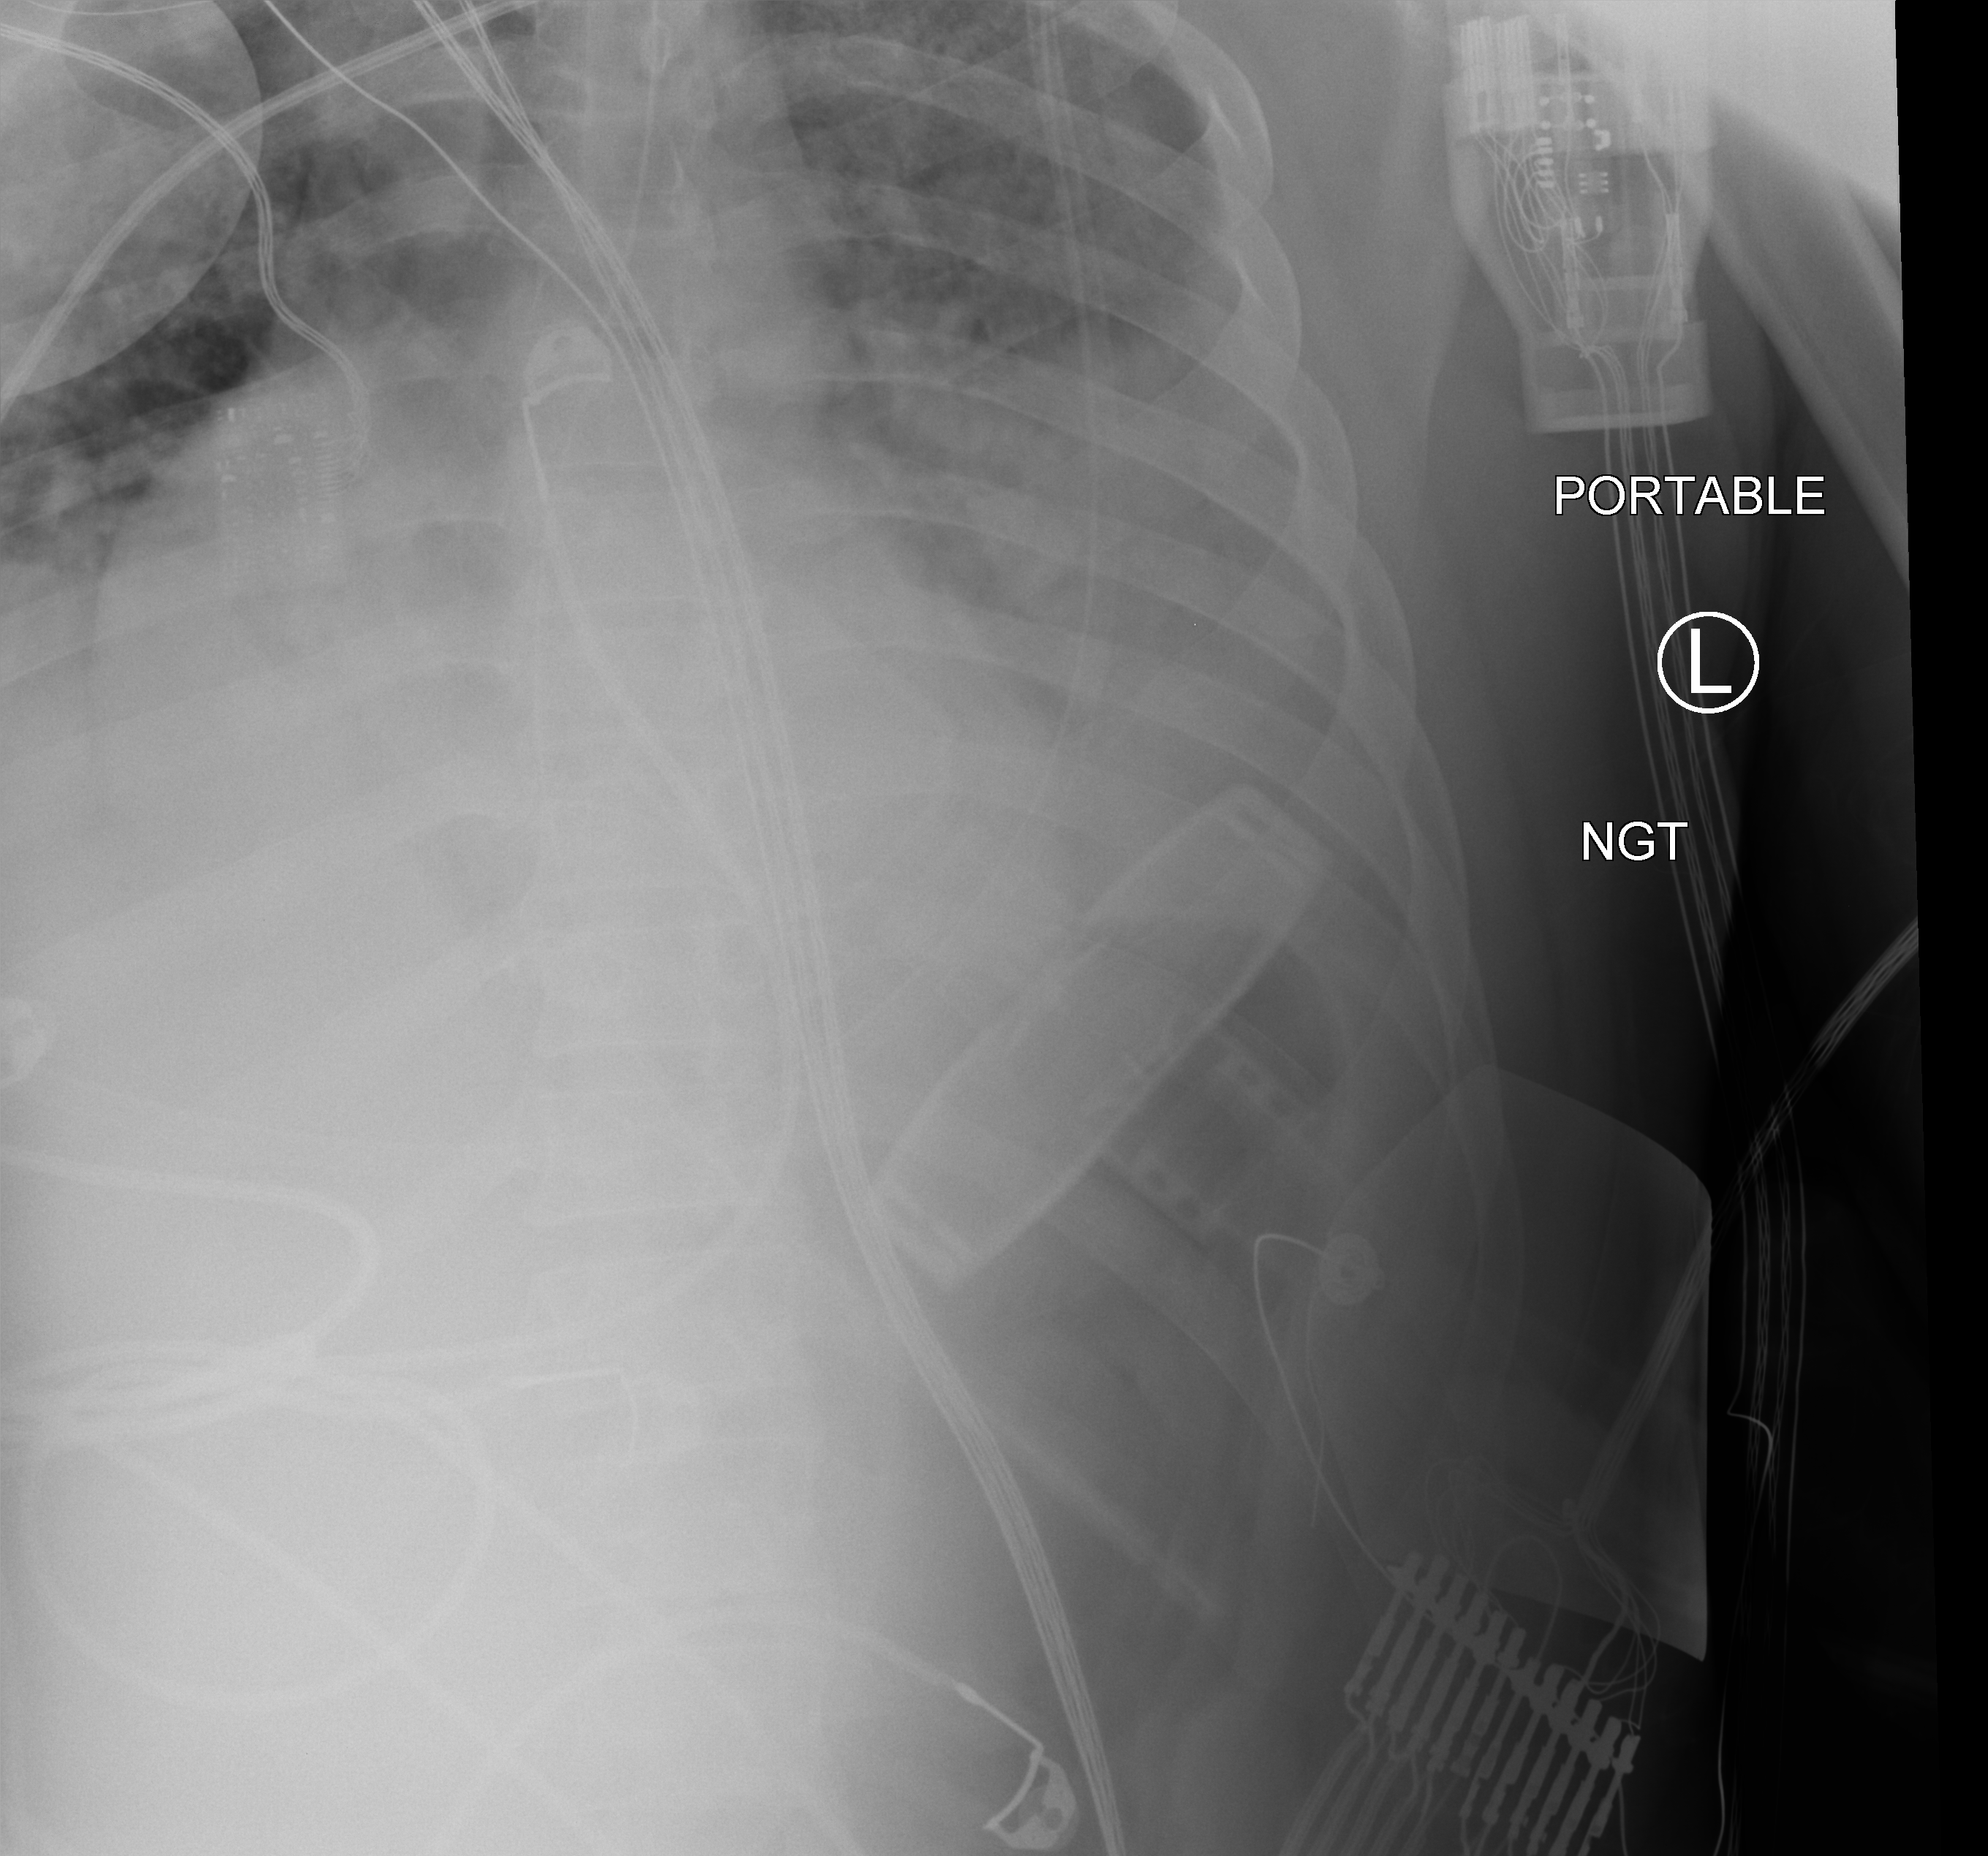
Bedside abdomen radiograph (computed radiography); anteroposterior (AP) projection. Male patient hospitalised with COVID-19, age 18–59 years.
Hospital-stay facts (about this admission, not read from this image; timing relative to this image not recorded): admitted to intensive care during this hospital stay: yes; mechanically ventilated during this hospital stay: yes.